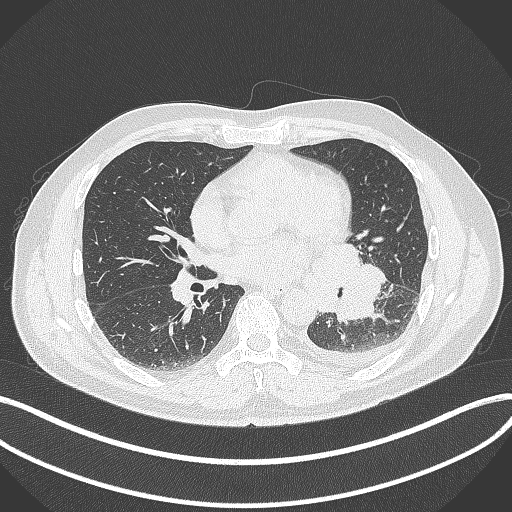
Chest CT, one axial slice; reconstruction kernel B70f; 120 kVp; lung window (W 1500 / L -600 HU); 512 × 512 image matrix, field of view 400 × 400 mm. Male patient, age 58 years. Case-level facts recorded for this patient, not image findings: clinical TNM (as recorded): T3 N1 M1b.
Outlined on this slice (rectangle marked by the reading radiologist):
- lung tumour (recorded histology: small cell carcinoma): bounding box (x1, y1, x2, y2) in pixels: (306, 243, 385, 327)